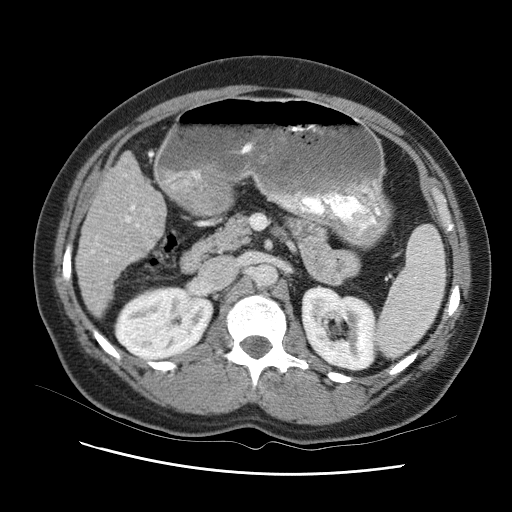
Contrast-enhanced abdominal CT (liver protocol), one axial slice. Position 39 of 95 along the scan axis. 120 kVp. One of 2 acquisitions stored at this slice position. Soft-tissue window (W 400 / L 40 HU). 512 × 512 image matrix. Case-level facts recorded for this patient, not image findings: diagnosis: hepatocellular carcinoma (patient treated with transarterial chemoembolisation; whether this scan precedes or follows treatment is not stated here); TNM stage (as recorded): Stage-I; Child-Pugh class: B; tumour differentiation: moderately differentiated; tumour nodularity: uninodular.
Outlined on this slice (semi-automatically segmented with operator editing):
- liver parenchyma outside the tumour (the mass and vessels are separate outlines, so this box may not span the whole liver): bounding box (x1, y1, x2, y2) in pixels: (76, 140, 170, 326)
- mass: (110, 260, 174, 303)
- liver vessels: (92, 198, 141, 293)